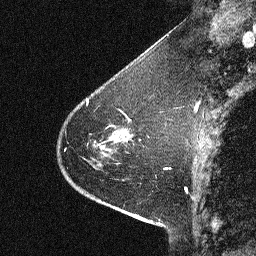
Breast MRI (dynamic contrast-enhanced), one sagittal slice. Dynamic contrast-enhanced study with each time point stored as its own series, time point 2 of 3 at this slice position (early post-contrast, ordered by acquisition time). 1.5 T. TE 4.5 ms, TR 11 ms. 2.06 mm slice thickness. 256 × 256 image matrix. Female patient, age 46 years. Case-level facts recorded for this patient, not image findings: setting: breast cancer imaged before/during neoadjuvant chemotherapy; receptor status: HER2-positive.
Annotated regions visible in this slice (semi-automatic segmentation, software-assisted and operator-edited):
- analysis volume of interest (the breast-tissue region the enhancement analysis was run in; not a lesion): bounding box [x1, y1, x2, y2] px = [42, 80, 150, 180]
- tumour enhancement mask (voxels above the 90 % enhancement threshold inside the analysis volume of interest): [92, 115, 125, 152]